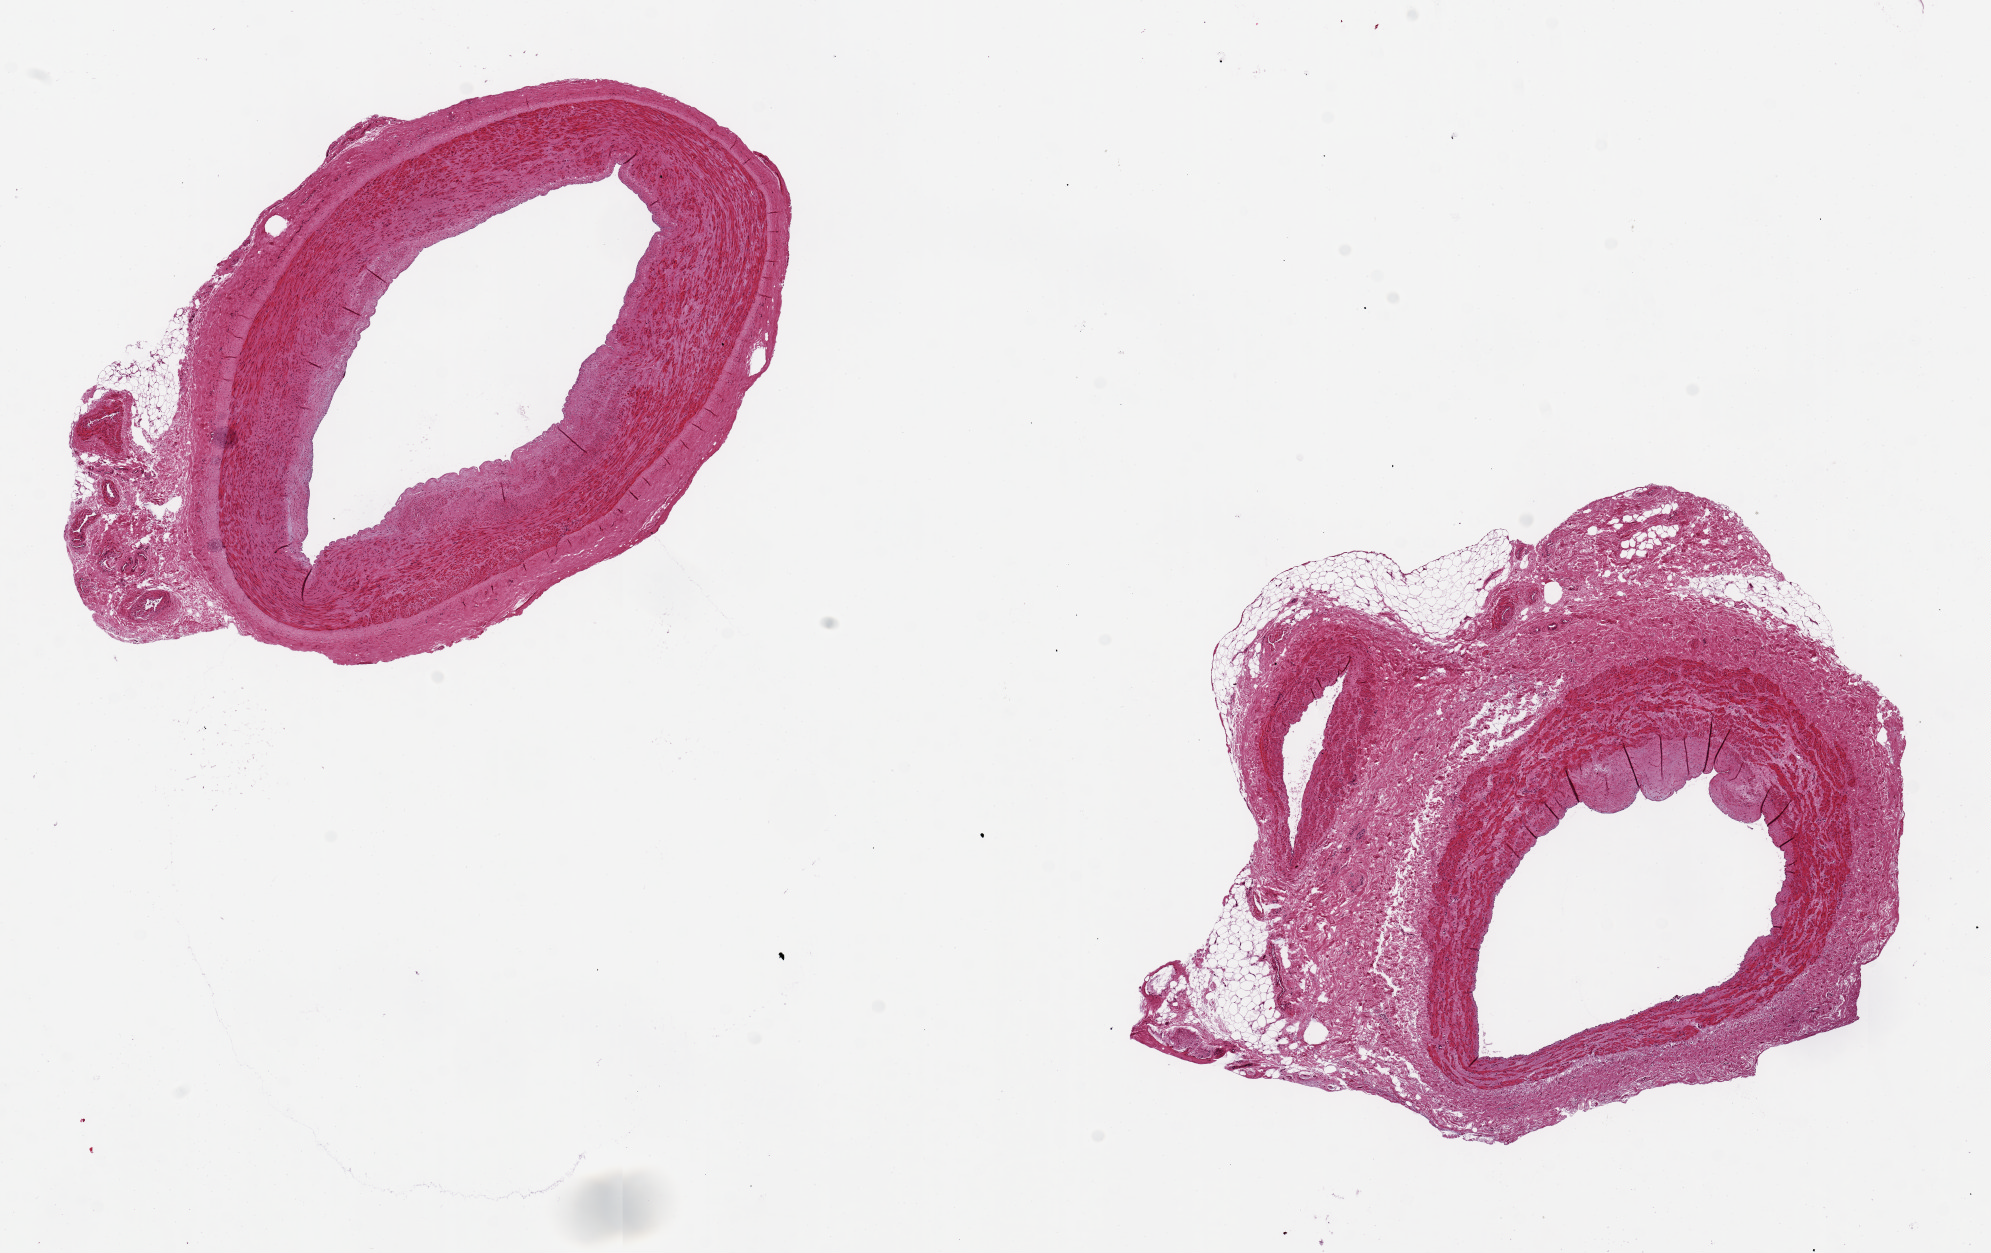
Haematoxylin and eosin whole-slide image, a low-resolution overview of the entire scanned area, about 15.8 x 9.9 mm. PAXgene-fixed, paraffin-embedded tissue. Section of tibial artery (target tissue). Donor tissue sample. Donor: female.
Pathologist's review note for this sample: 2 pieces ~4.5mm d generally clean specimen, trace adherent fat/fibrous tissue.